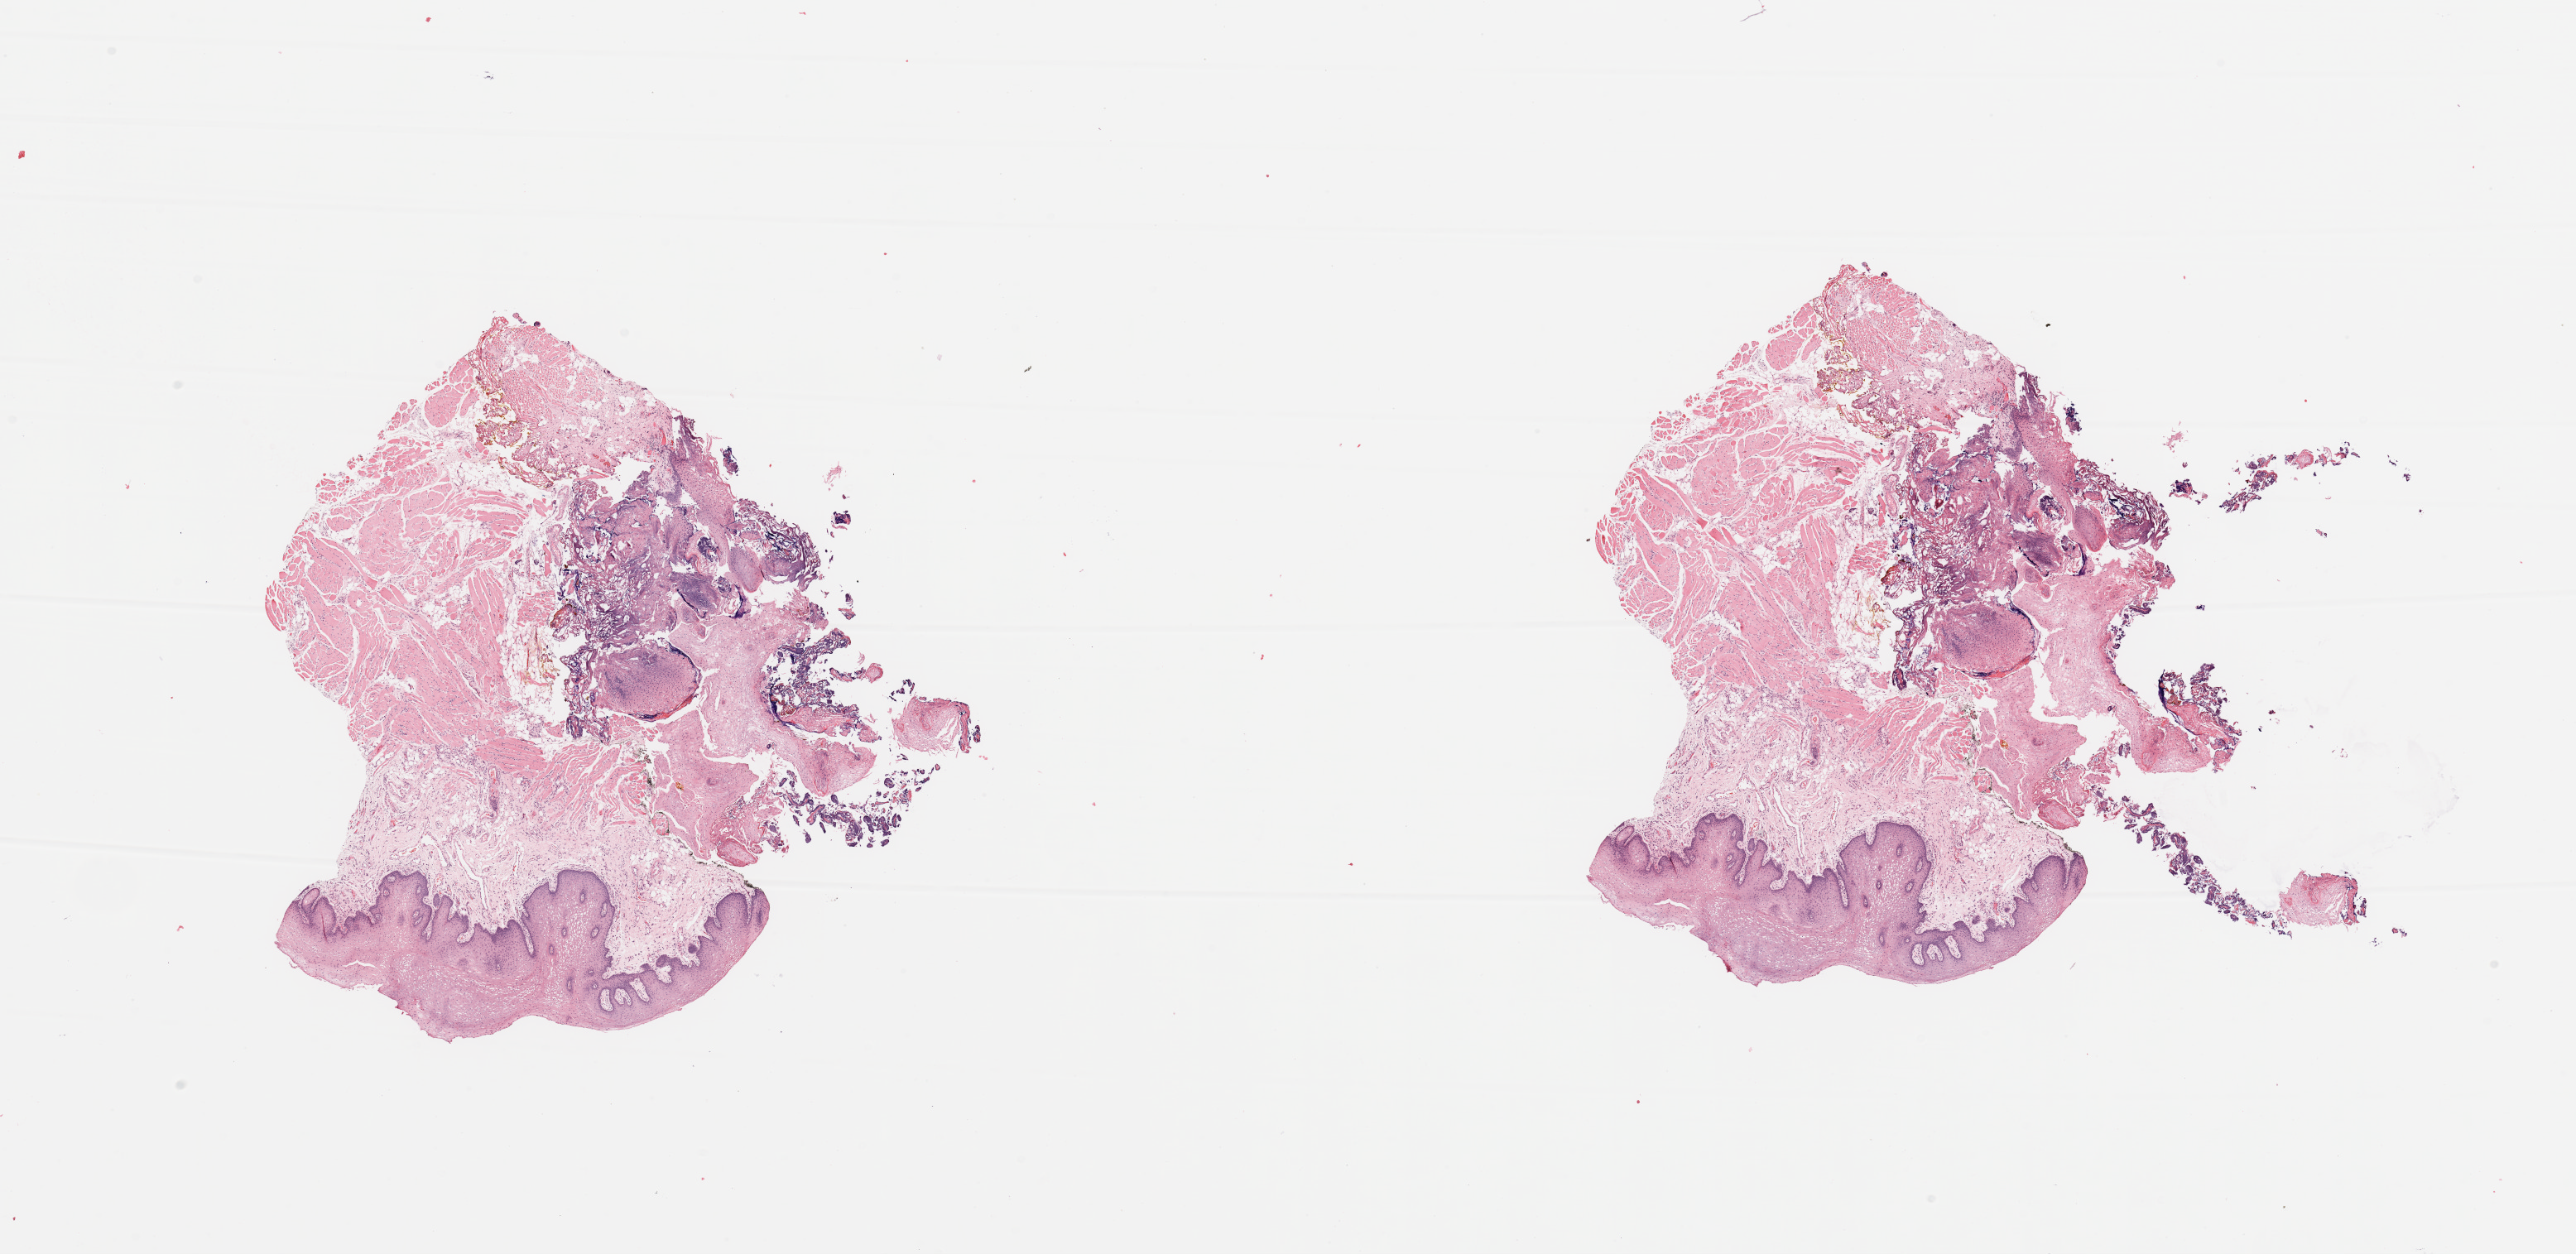
Hematoxylin and eosin (H&E) stained whole-slide image, low-resolution overview of the scanned area, about 24.6 x 12.0 mm, normal (non-tumour) tissue sample, sampled site: tongue. Patient: male, age 77 years.
This section: normal (non-tumour) tissue from the same patient. Patient diagnosis: Squamous cell carcinoma, NOS (tongue, NOS).